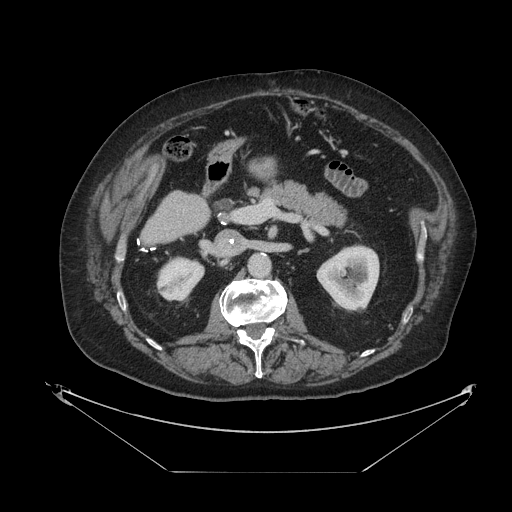
Contrast-enhanced abdominal CT, one axial slice; position 41 of 121 along the scan axis; 120 kVp; intravenous contrast given; soft-tissue window (W 400 / L 40 HU); 2.5 mm slice thickness; 512 × 512 image matrix, field of view 500 × 500 mm. Male patient, age 68 years. Case-level facts recorded for this patient, not image findings: diagnosis: colorectal cancer liver metastases, imaged before liver resection; multiple liver metastases: no; largest metastasis: 4 cm.
Annotated regions visible in this slice (outlined manually by an expert reader):
- liver: bounding box (x1, y1, x2, y2) in pixels: (144, 192, 209, 243)
- planned liver remnant (the part of the liver to remain after resection): (144, 192, 209, 243)